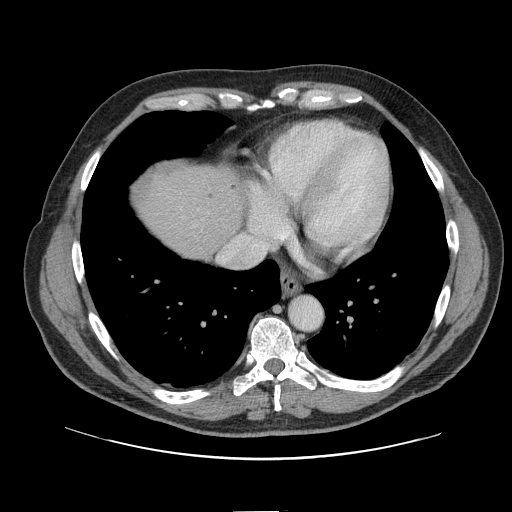
Contrast-enhanced abdominal CT, one axial slice; slice 139 of 161 in the series (ordered by position); intravenous contrast given; soft-tissue window (W 400 / L 40 HU); 2.5 mm slice thickness; 512 × 512 image matrix. Male patient, age 66 years. Case-level facts recorded for this patient, not image findings: diagnosis: colorectal cancer liver metastases, imaged before liver resection; multiple liver metastases: no; largest metastasis: 3.5 cm; chemotherapy before resection: yes.
Outlined on this slice (outlined manually by an expert reader):
- hepatic veins: box from (x=218, y=236) to (x=241, y=263) px
- liver: (x=138, y=167)–(x=242, y=258)
- planned liver remnant (the part of the liver to remain after resection): (x=137, y=168)–(x=242, y=259)
- liver metastasis: (x=231, y=185)–(x=237, y=192)
- liver metastasis: (x=210, y=195)–(x=217, y=200)